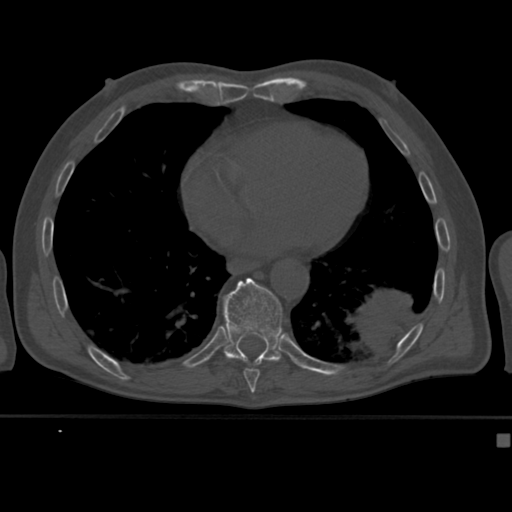
CT including the spine, one axial slice. Slice 236 of 430 in the series (ordered by position). 120 kVp. Bone window (W 1800 / L 400 HU). 1.5 mm slice thickness. 512 × 512 image matrix, field of view 337 × 337 mm. Patient: male, 64 years. Case-level facts recorded for this patient, not image findings: primary cancer: uterus; vertebrae with lytic lesions (as recorded): T1, T4, T5, T7, L5.
Structures marked on this image (semi-automatic segmentation, software-assisted and operator-edited):
- T10 vertebra: bounding box (x1, y1, x2, y2) in pixels: (223, 278, 282, 366)
- T9 vertebra: (243, 369, 260, 382)